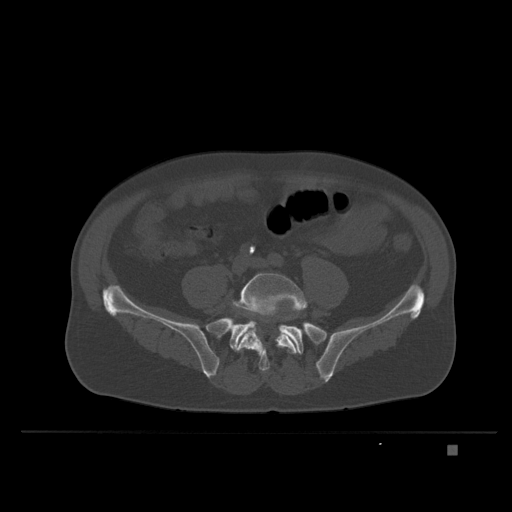
CT including the spine, one axial slice; position 51 of 435 along the scan axis; bone window (W 1800 / L 400 HU); 1.5 mm slice thickness; 512 × 512 image matrix. Male patient, age 73 years. Case-level facts recorded for this patient, not image findings: primary cancer: skin.
Annotated regions visible in this slice (semi-automatic segmentation, software-assisted and operator-edited):
- L5 vertebra: bounding box (x1, y1, x2, y2) in pixels: (237, 273, 306, 373)